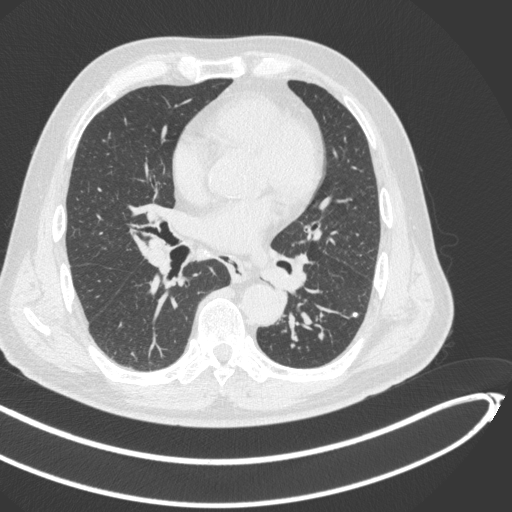
Chest CT, one axial slice. Slice 235 of 466 in the series (ordered by position). Lung window (W 1500 / L -600 HU). 1 mm slice thickness. 512 × 512 image matrix, field of view 400 × 400 mm. Patient: male, 64 years. Case-level facts recorded for this patient, not image findings: clinical TNM (as recorded): T1c N0 M0.
Structures marked on this image (rectangle marked by the reading radiologist):
- lung tumour (recorded histology: squamous cell carcinoma): box from (x=260, y=255) to (x=301, y=291) px